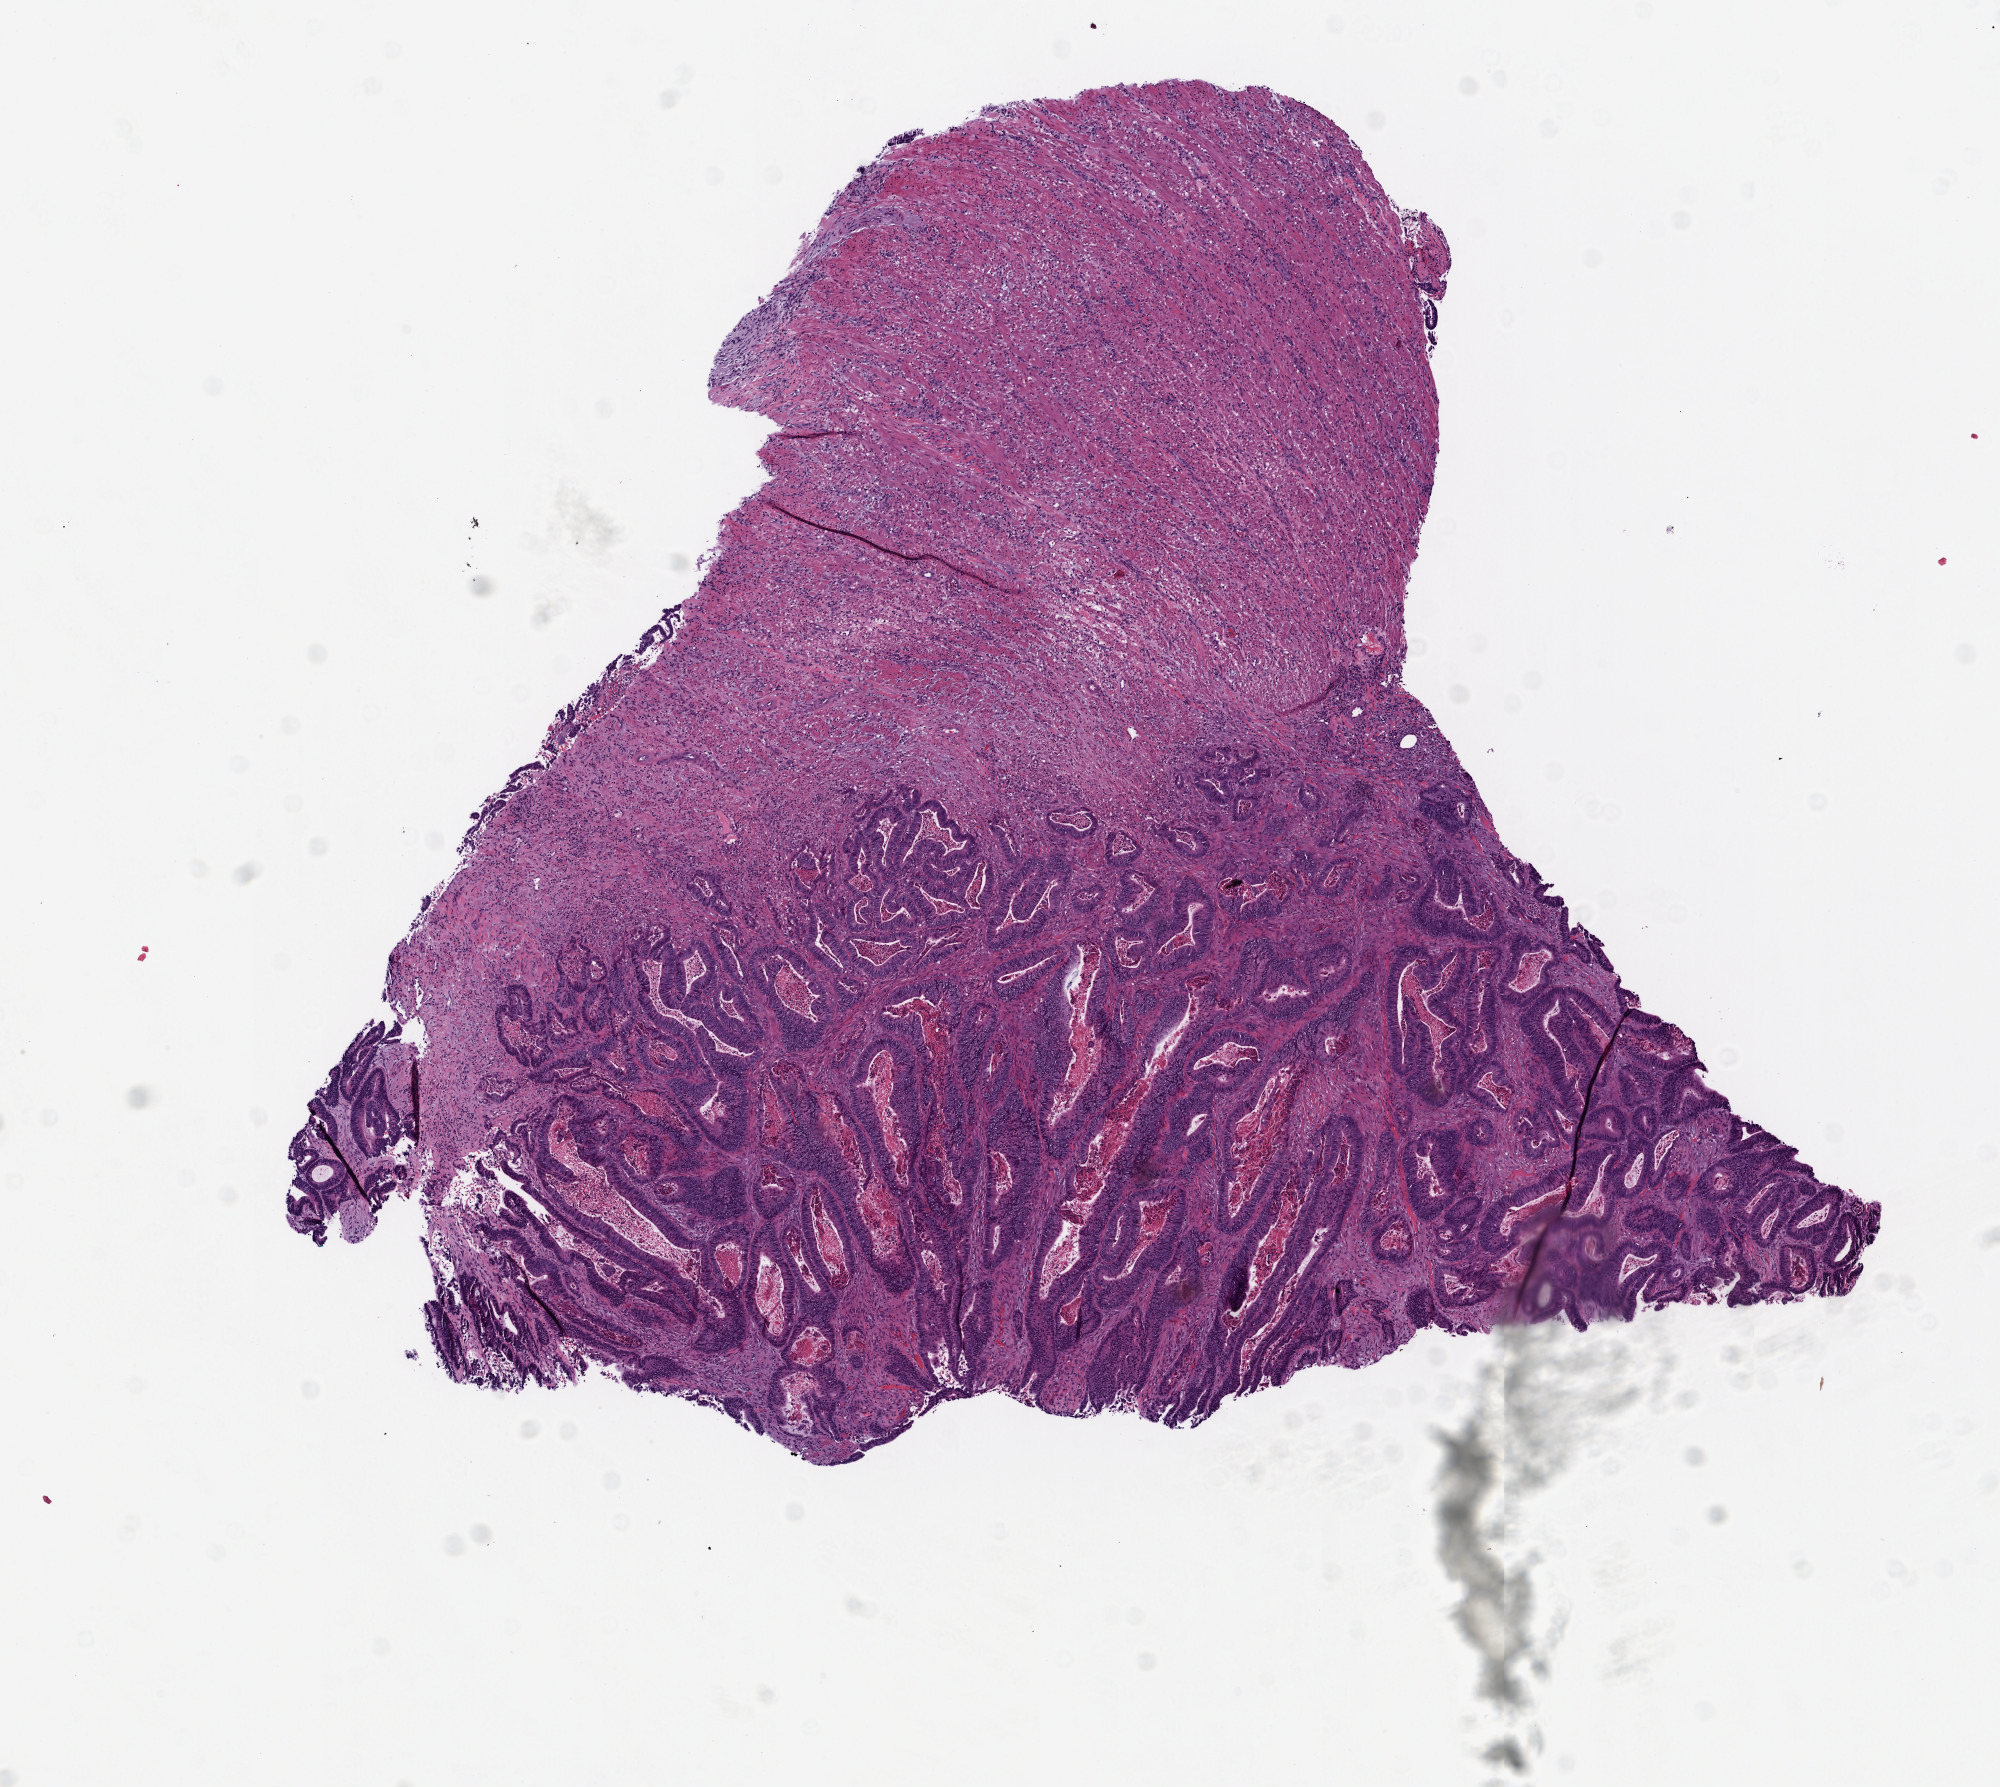
H&E whole-slide image, shown as a low-resolution overview of the whole scanned area (about 8.0 x 7.2 mm); frozen section from the top of the tissue portion; colon, primary tumour sample. Patient: male, age at initial diagnosis 62 years. Composition of this section per pathologist review: tumour cells 25%, tumour nuclei 75%, normal cells 50%, stromal cells 10%, necrosis 15%.
Lymph nodes positive (case pathology): 0 of 30 examined. TNM: T3 N0 M0. Diagnosis: Adenocarcinoma, NOS. AJCC pathologic stage: IIA.